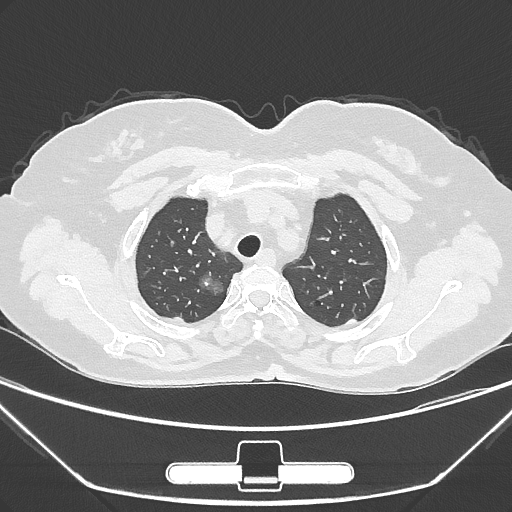
Chest CT, one axial slice; slice 232 of 275 in the series (ordered by position); reconstruction kernel IMR1,SharpPlus; 120 kVp; lung window (W 1500 / L -600 HU); 512 × 512 image matrix, field of view 356 × 356 mm. Patient: female, 63 years. From the clinical record (not read from this slice): clinical TNM (as recorded): T1a N0 M0.
Annotated regions visible in this slice (bounding box drawn by a radiologist):
- lung tumour (recorded histology: adenocarcinoma): box from (x=190, y=265) to (x=223, y=303) px